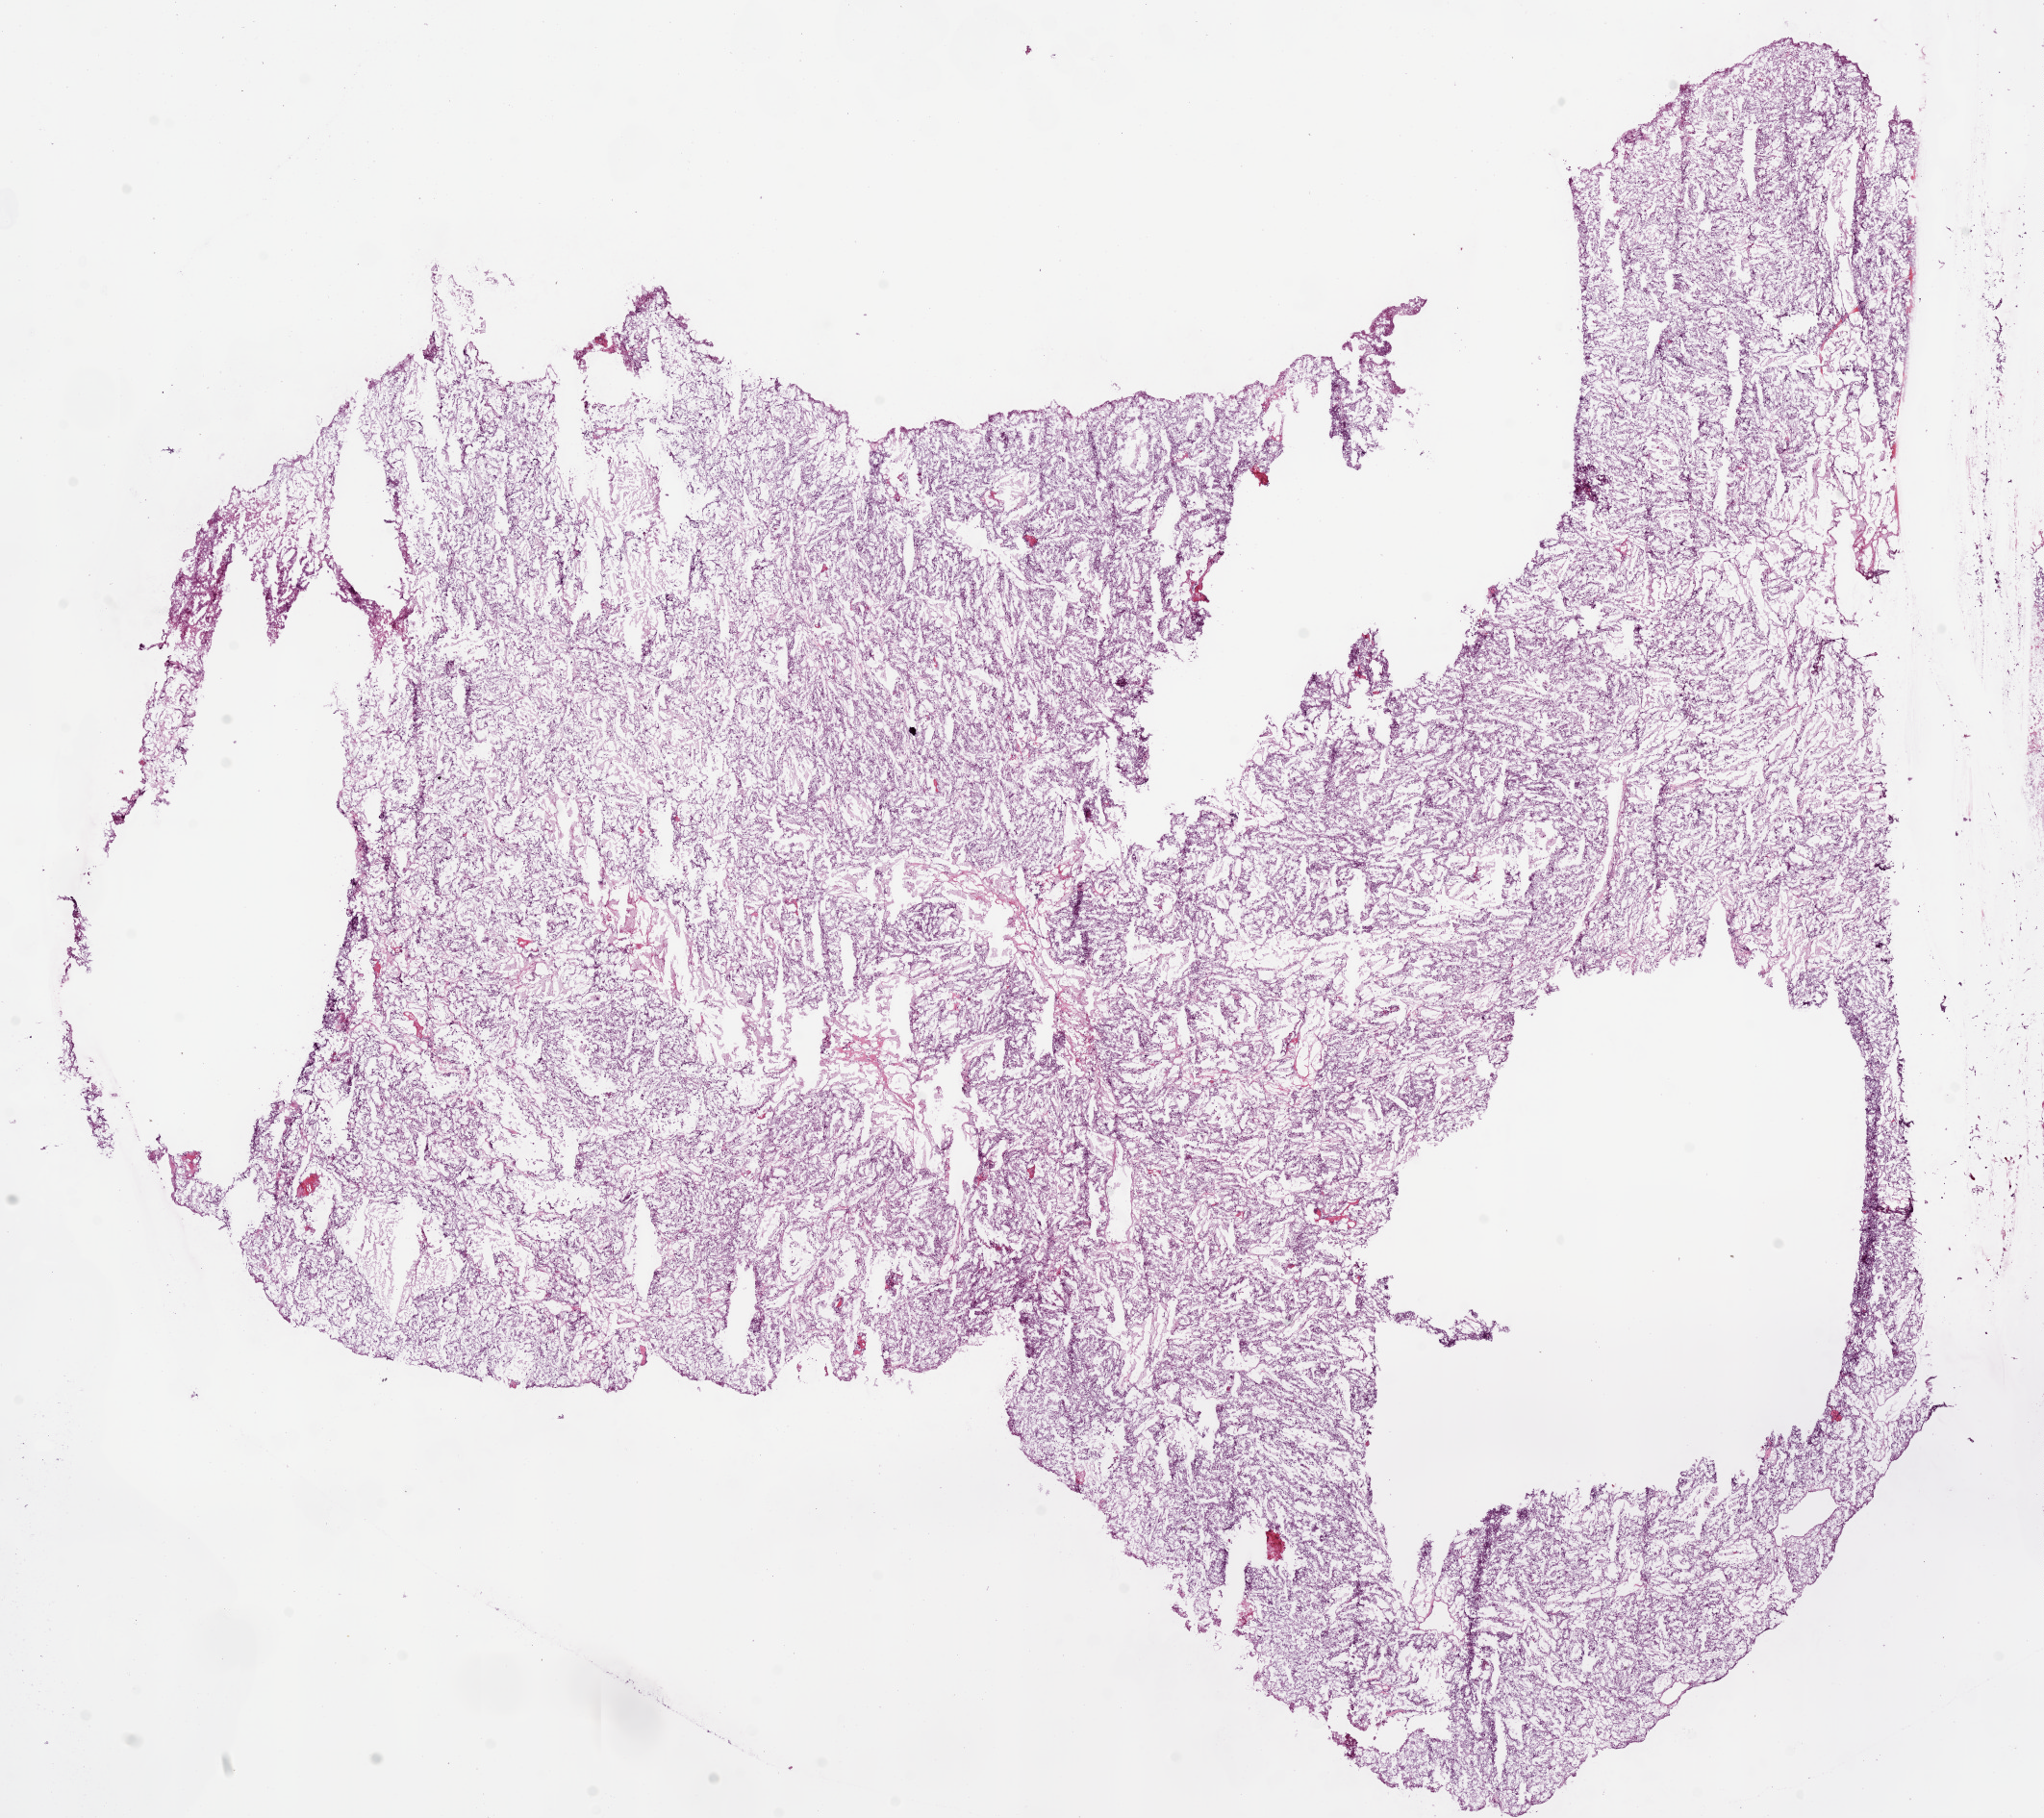
Digitized Hematoxylin and eosin (H&E) stained tissue section (whole slide) — shown as a low-resolution overview of the whole scanned area (about 17.1 x 15.2 mm); frozen section from the bottom of the tissue portion; sample: primary tumour, kidney. Male, age 83 years at initial diagnosis. Histologic grade: G3 (poorly differentiated). Pathologist review of this section (percent, as recorded): tumour cells 90%, tumour nuclei 90%, normal cells 0%, stromal cells 10%, necrosis 0%.
AJCC pathologic stage: IV. Diagnosis: Clear cell adenocarcinoma, NOS.